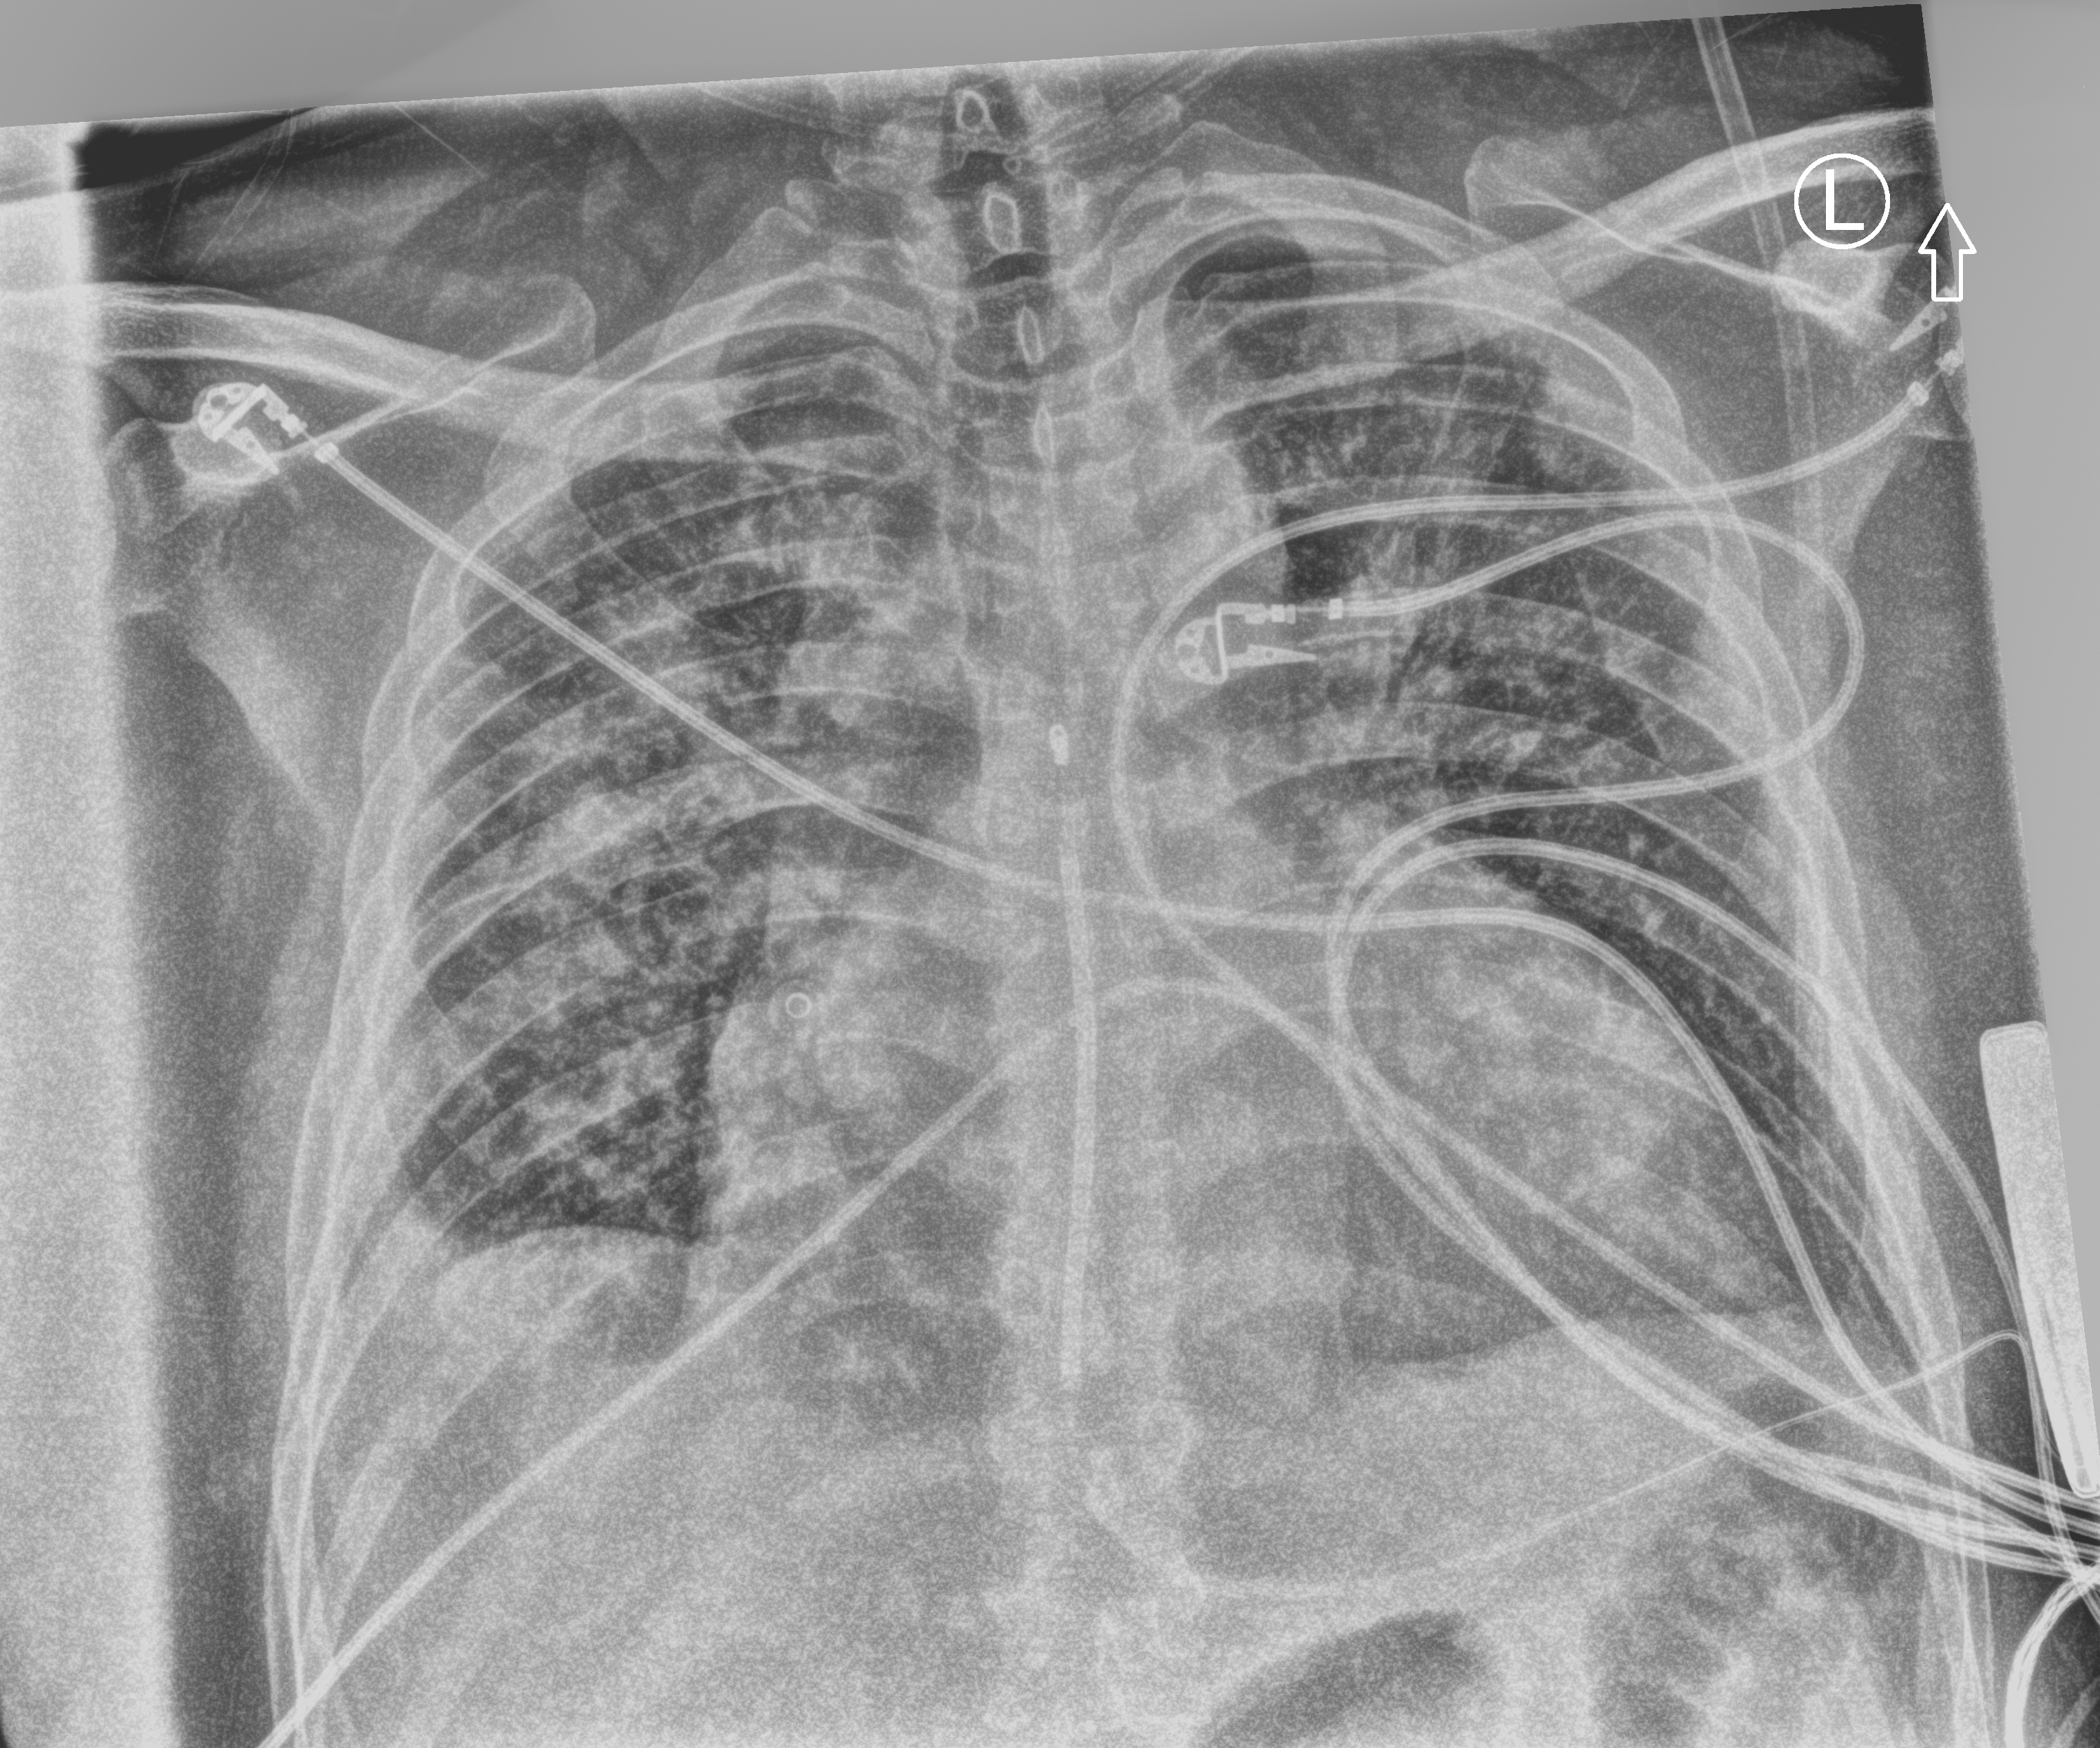
Portable chest radiograph. Patient hospitalised with COVID-19; male, aged 18–59 years.
Admission-level facts for this patient (not findings on this image; timing relative to this image not recorded): diabetes (admission record): no; admitted to intensive care during this hospital stay: no; hypertension (admission record): yes.